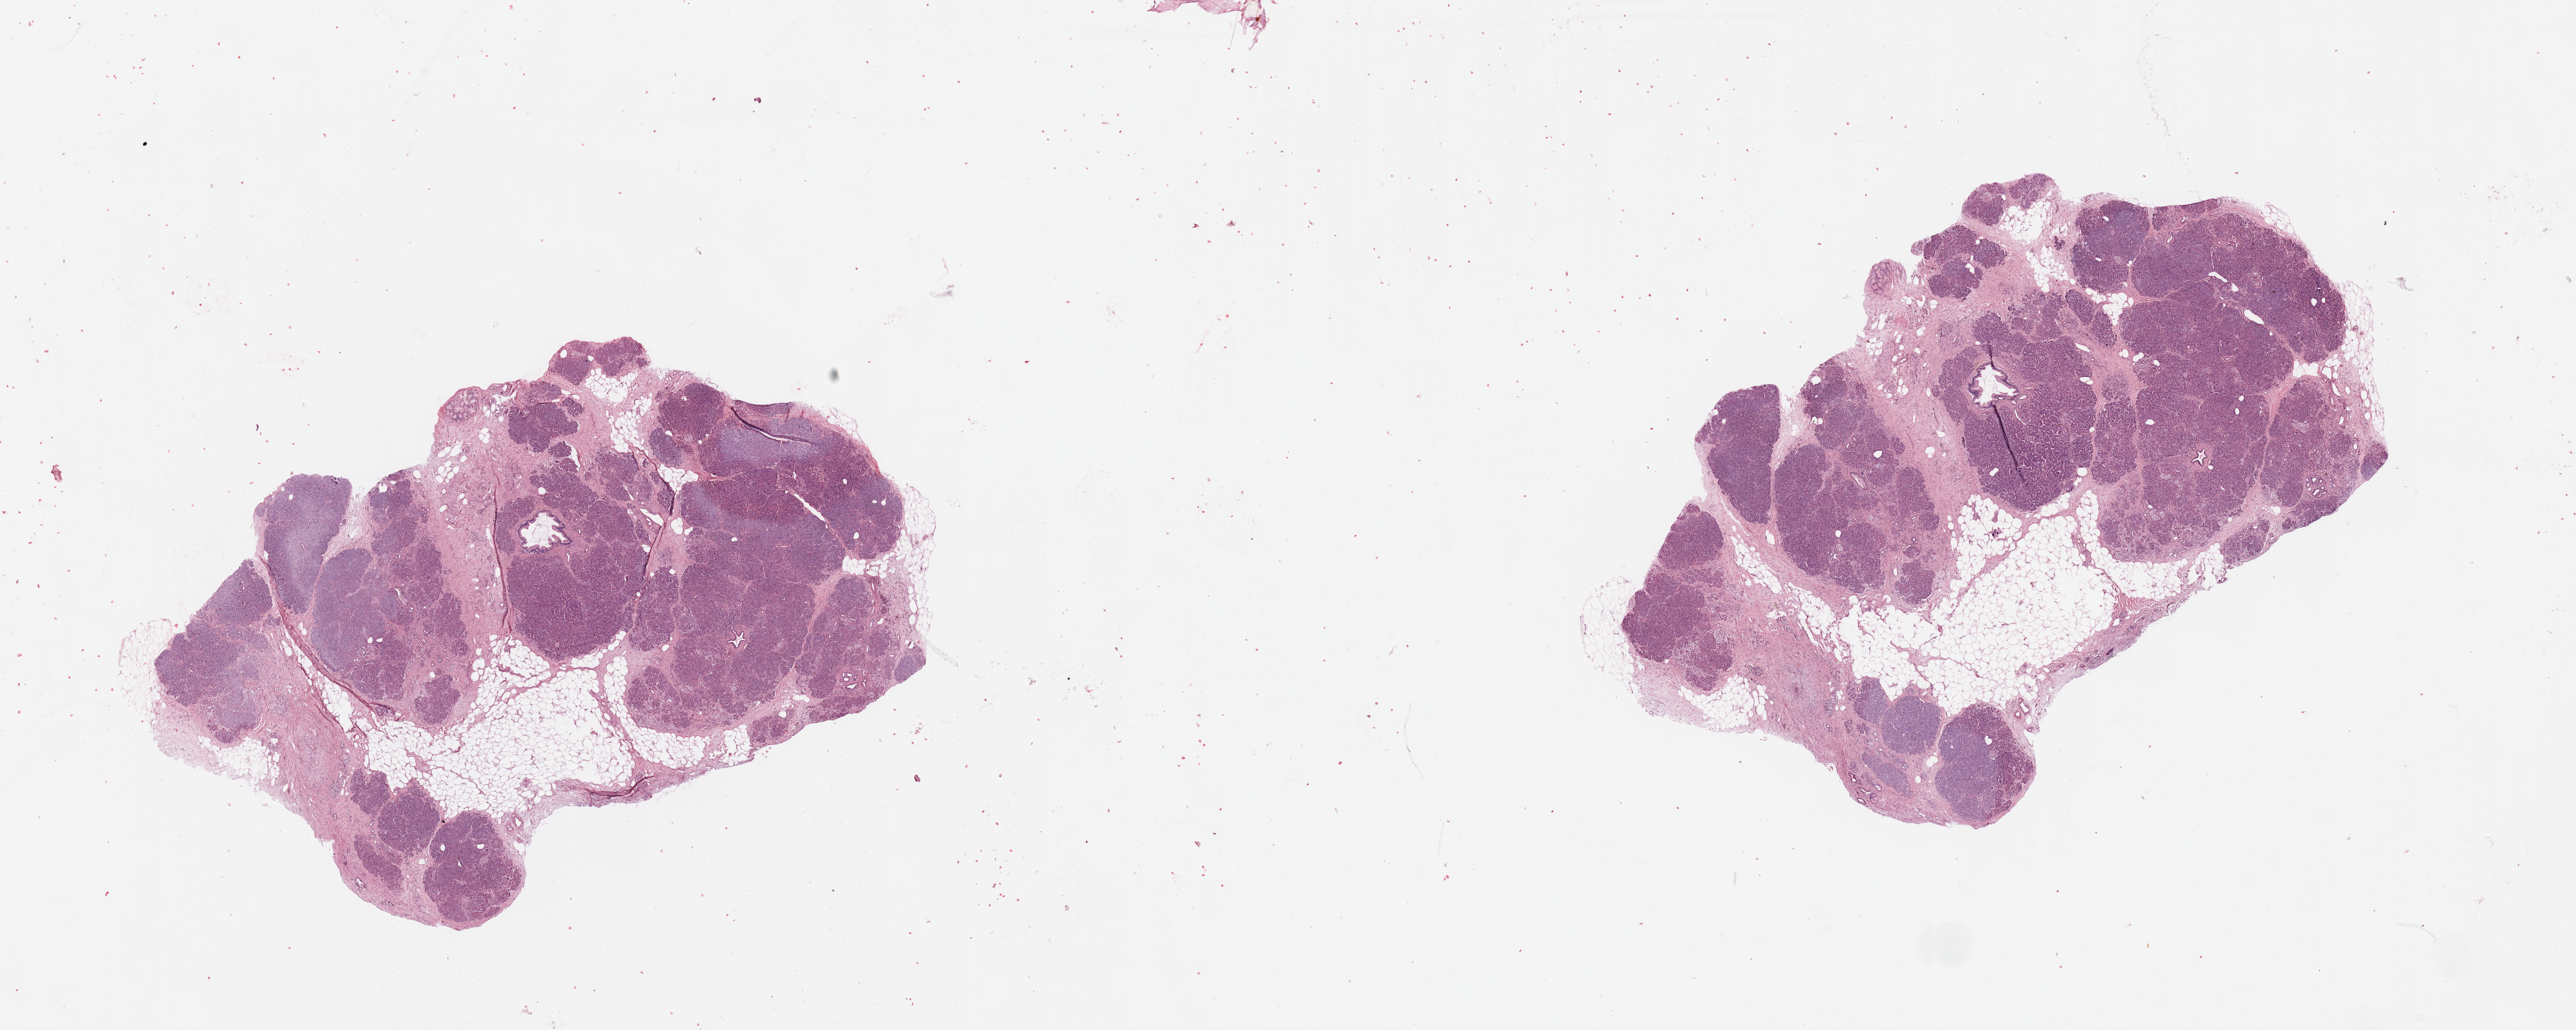
Whole-slide histology image, H&E — shown as a low-resolution overview of the whole scanned area (about 31.5 x 12.6 mm). Pancreas, tissue type not recorded.
Patient diagnosis (cohort enrolment): ductal adenocarcinoma (pancreas).